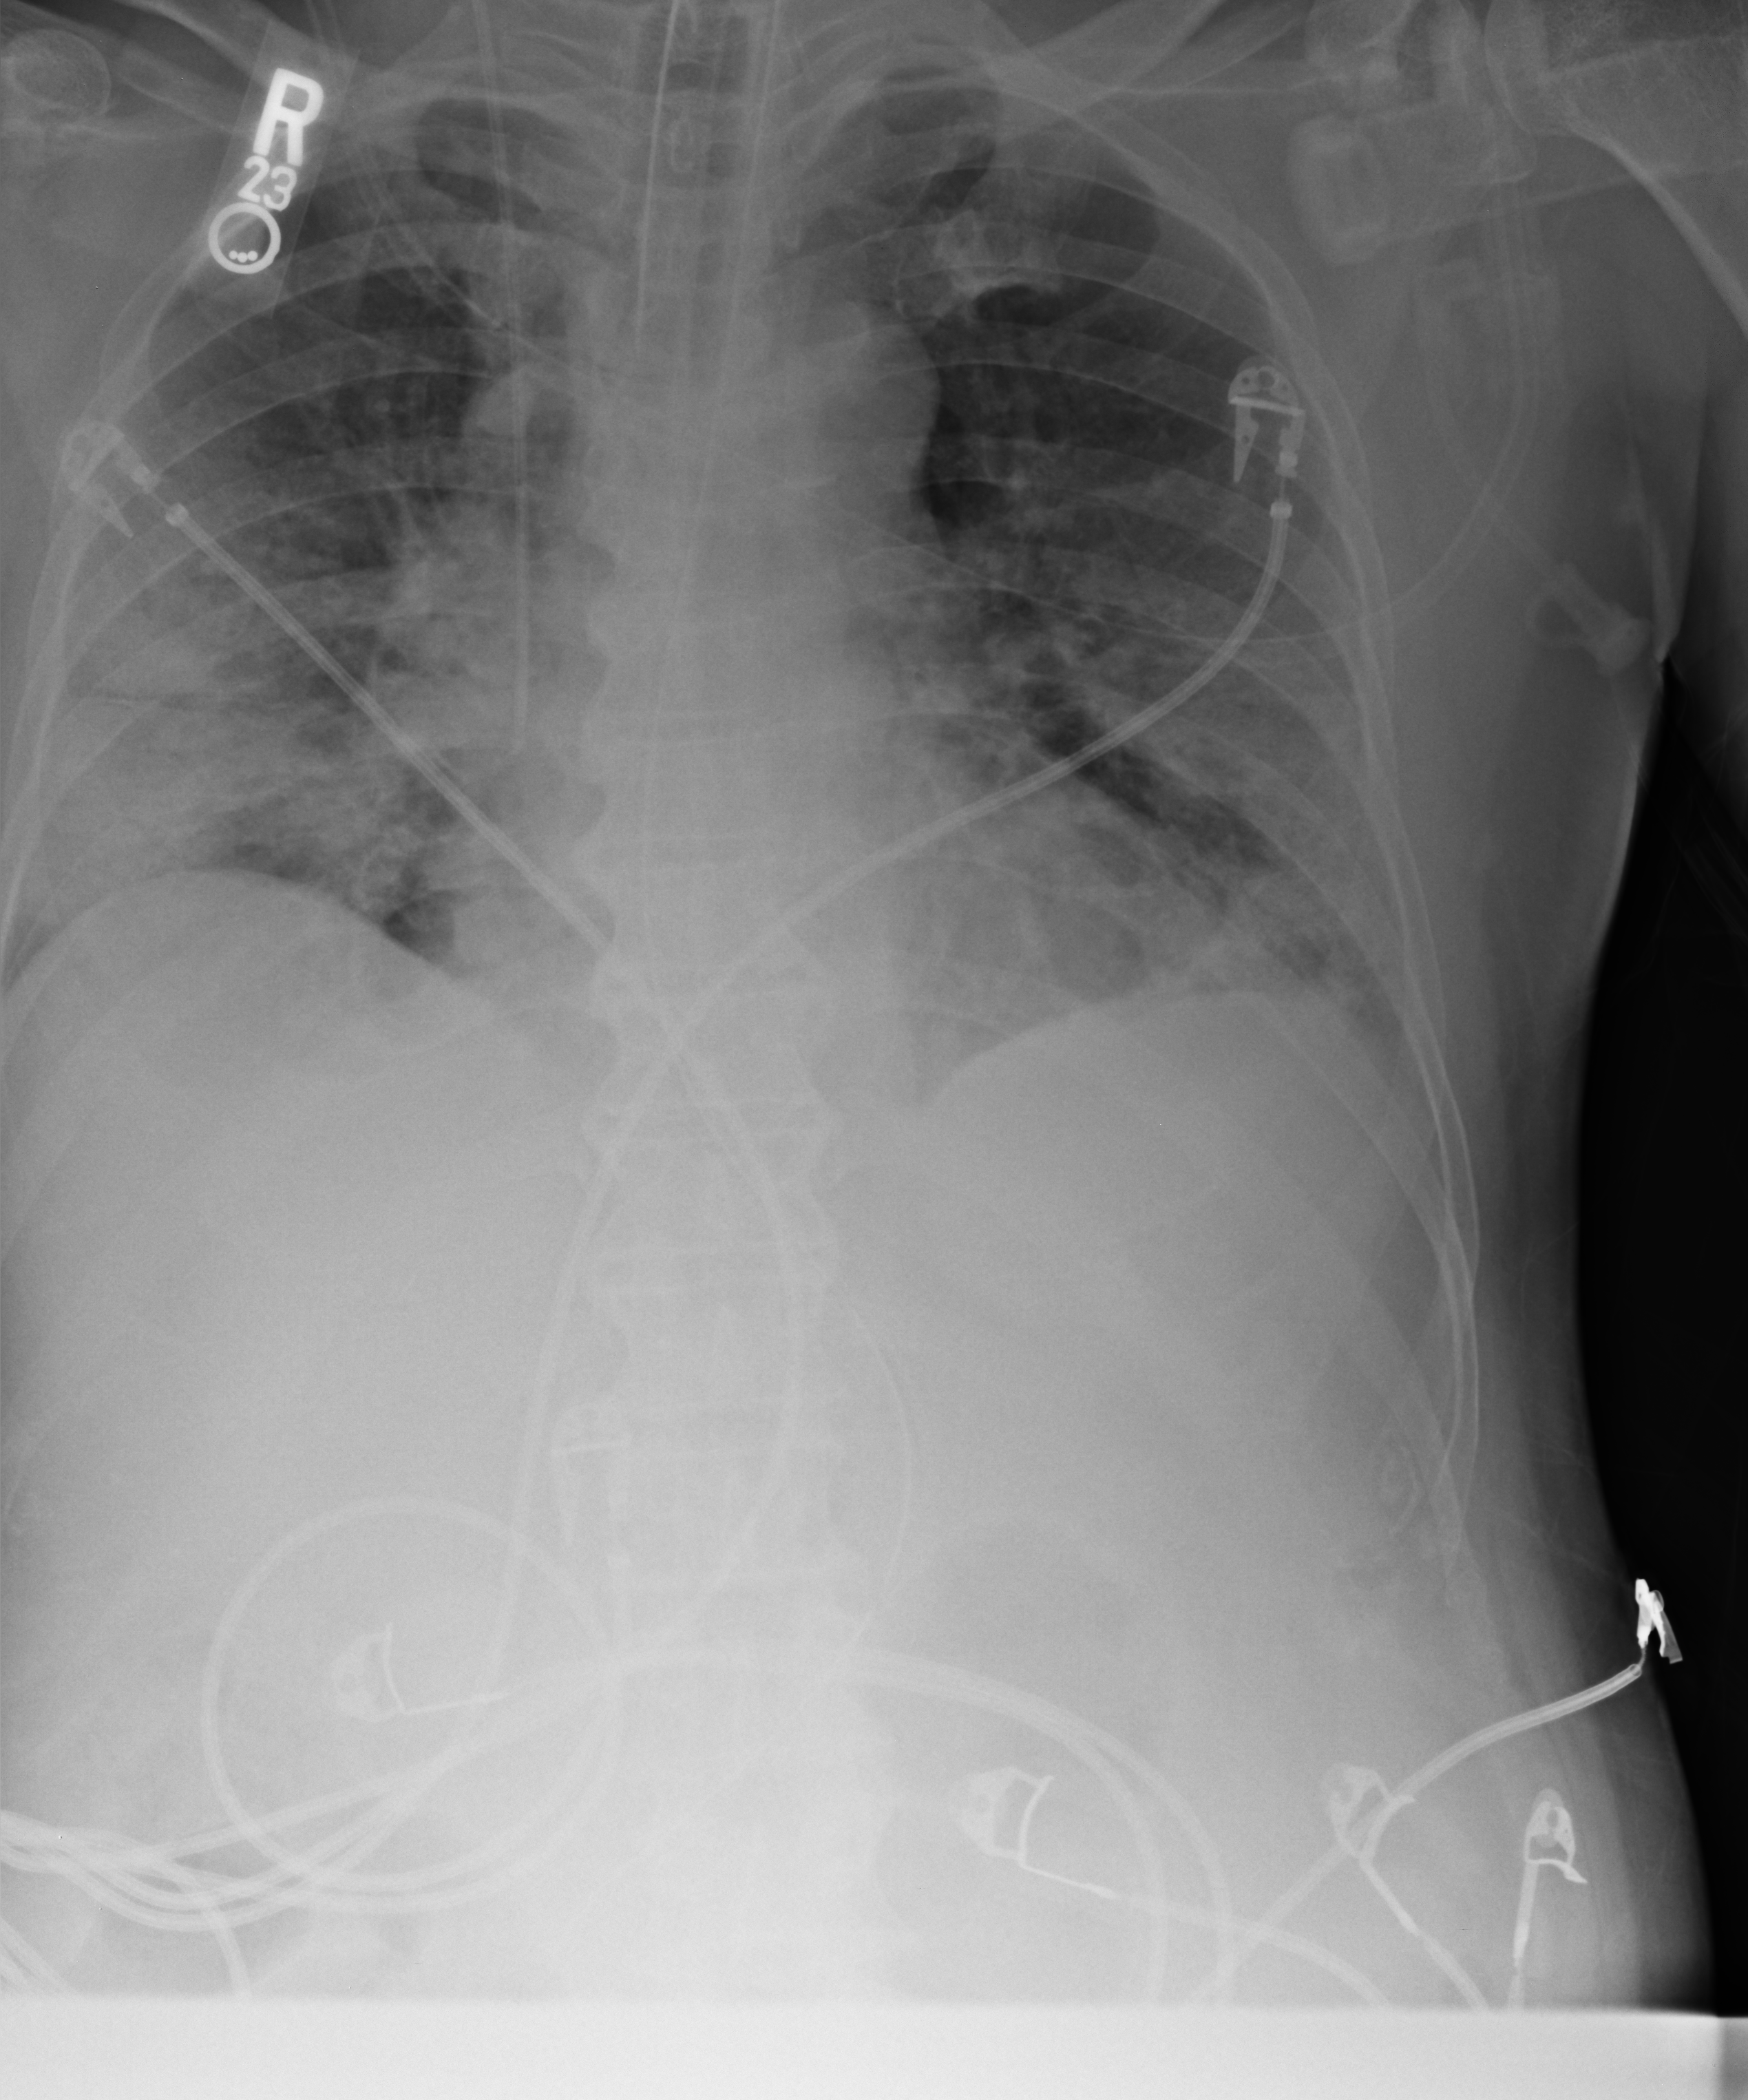
Bedside chest radiograph (computed radiography); anteroposterior (AP) projection. Male patient hospitalised with COVID-19, age 60–74 years.
Hospital-stay facts (about this admission, not read from this image; timing relative to this image not recorded):
- COPD (admission record): no